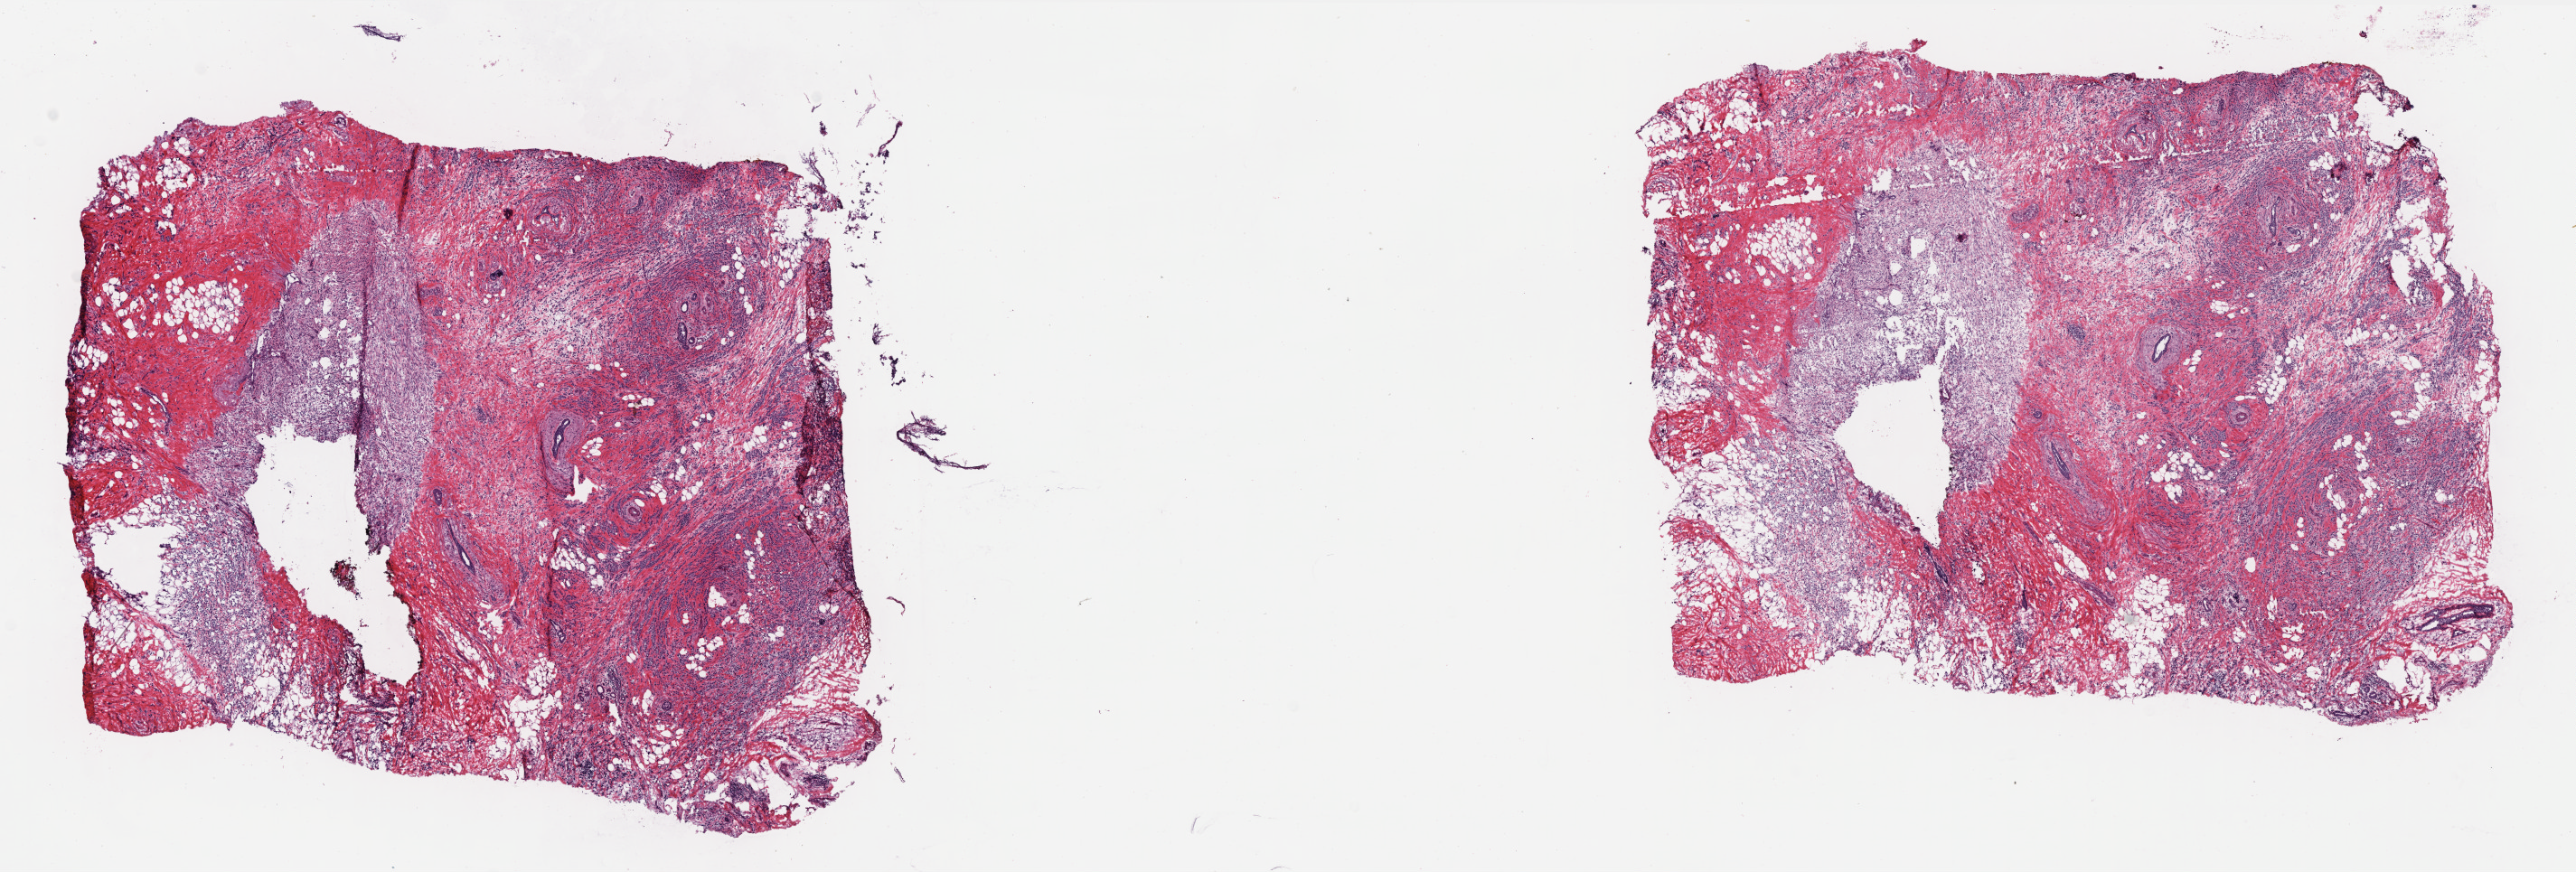
H&E whole-slide image — shown as a low-resolution overview of the whole scanned area (about 22.8 x 7.7 mm), frozen section from the top of the tissue portion, sample: primary tumour, breast. Female patient; age at initial diagnosis 78 years. Composition of this section per pathologist review: tumour cells 65%, tumour nuclei 75%, normal cells 18%, stromal cells 15%, necrosis 2%. Inflammatory infiltration, as recorded: lymphocyte infiltration 17%, monocyte infiltration 0%, neutrophil infiltration 0%.
Laterality: right. AJCC pathologic stage: IIA. Lymph nodes positive (case pathology): 0 of 5 examined. Diagnosis: Infiltrating duct and lobular carcinoma.